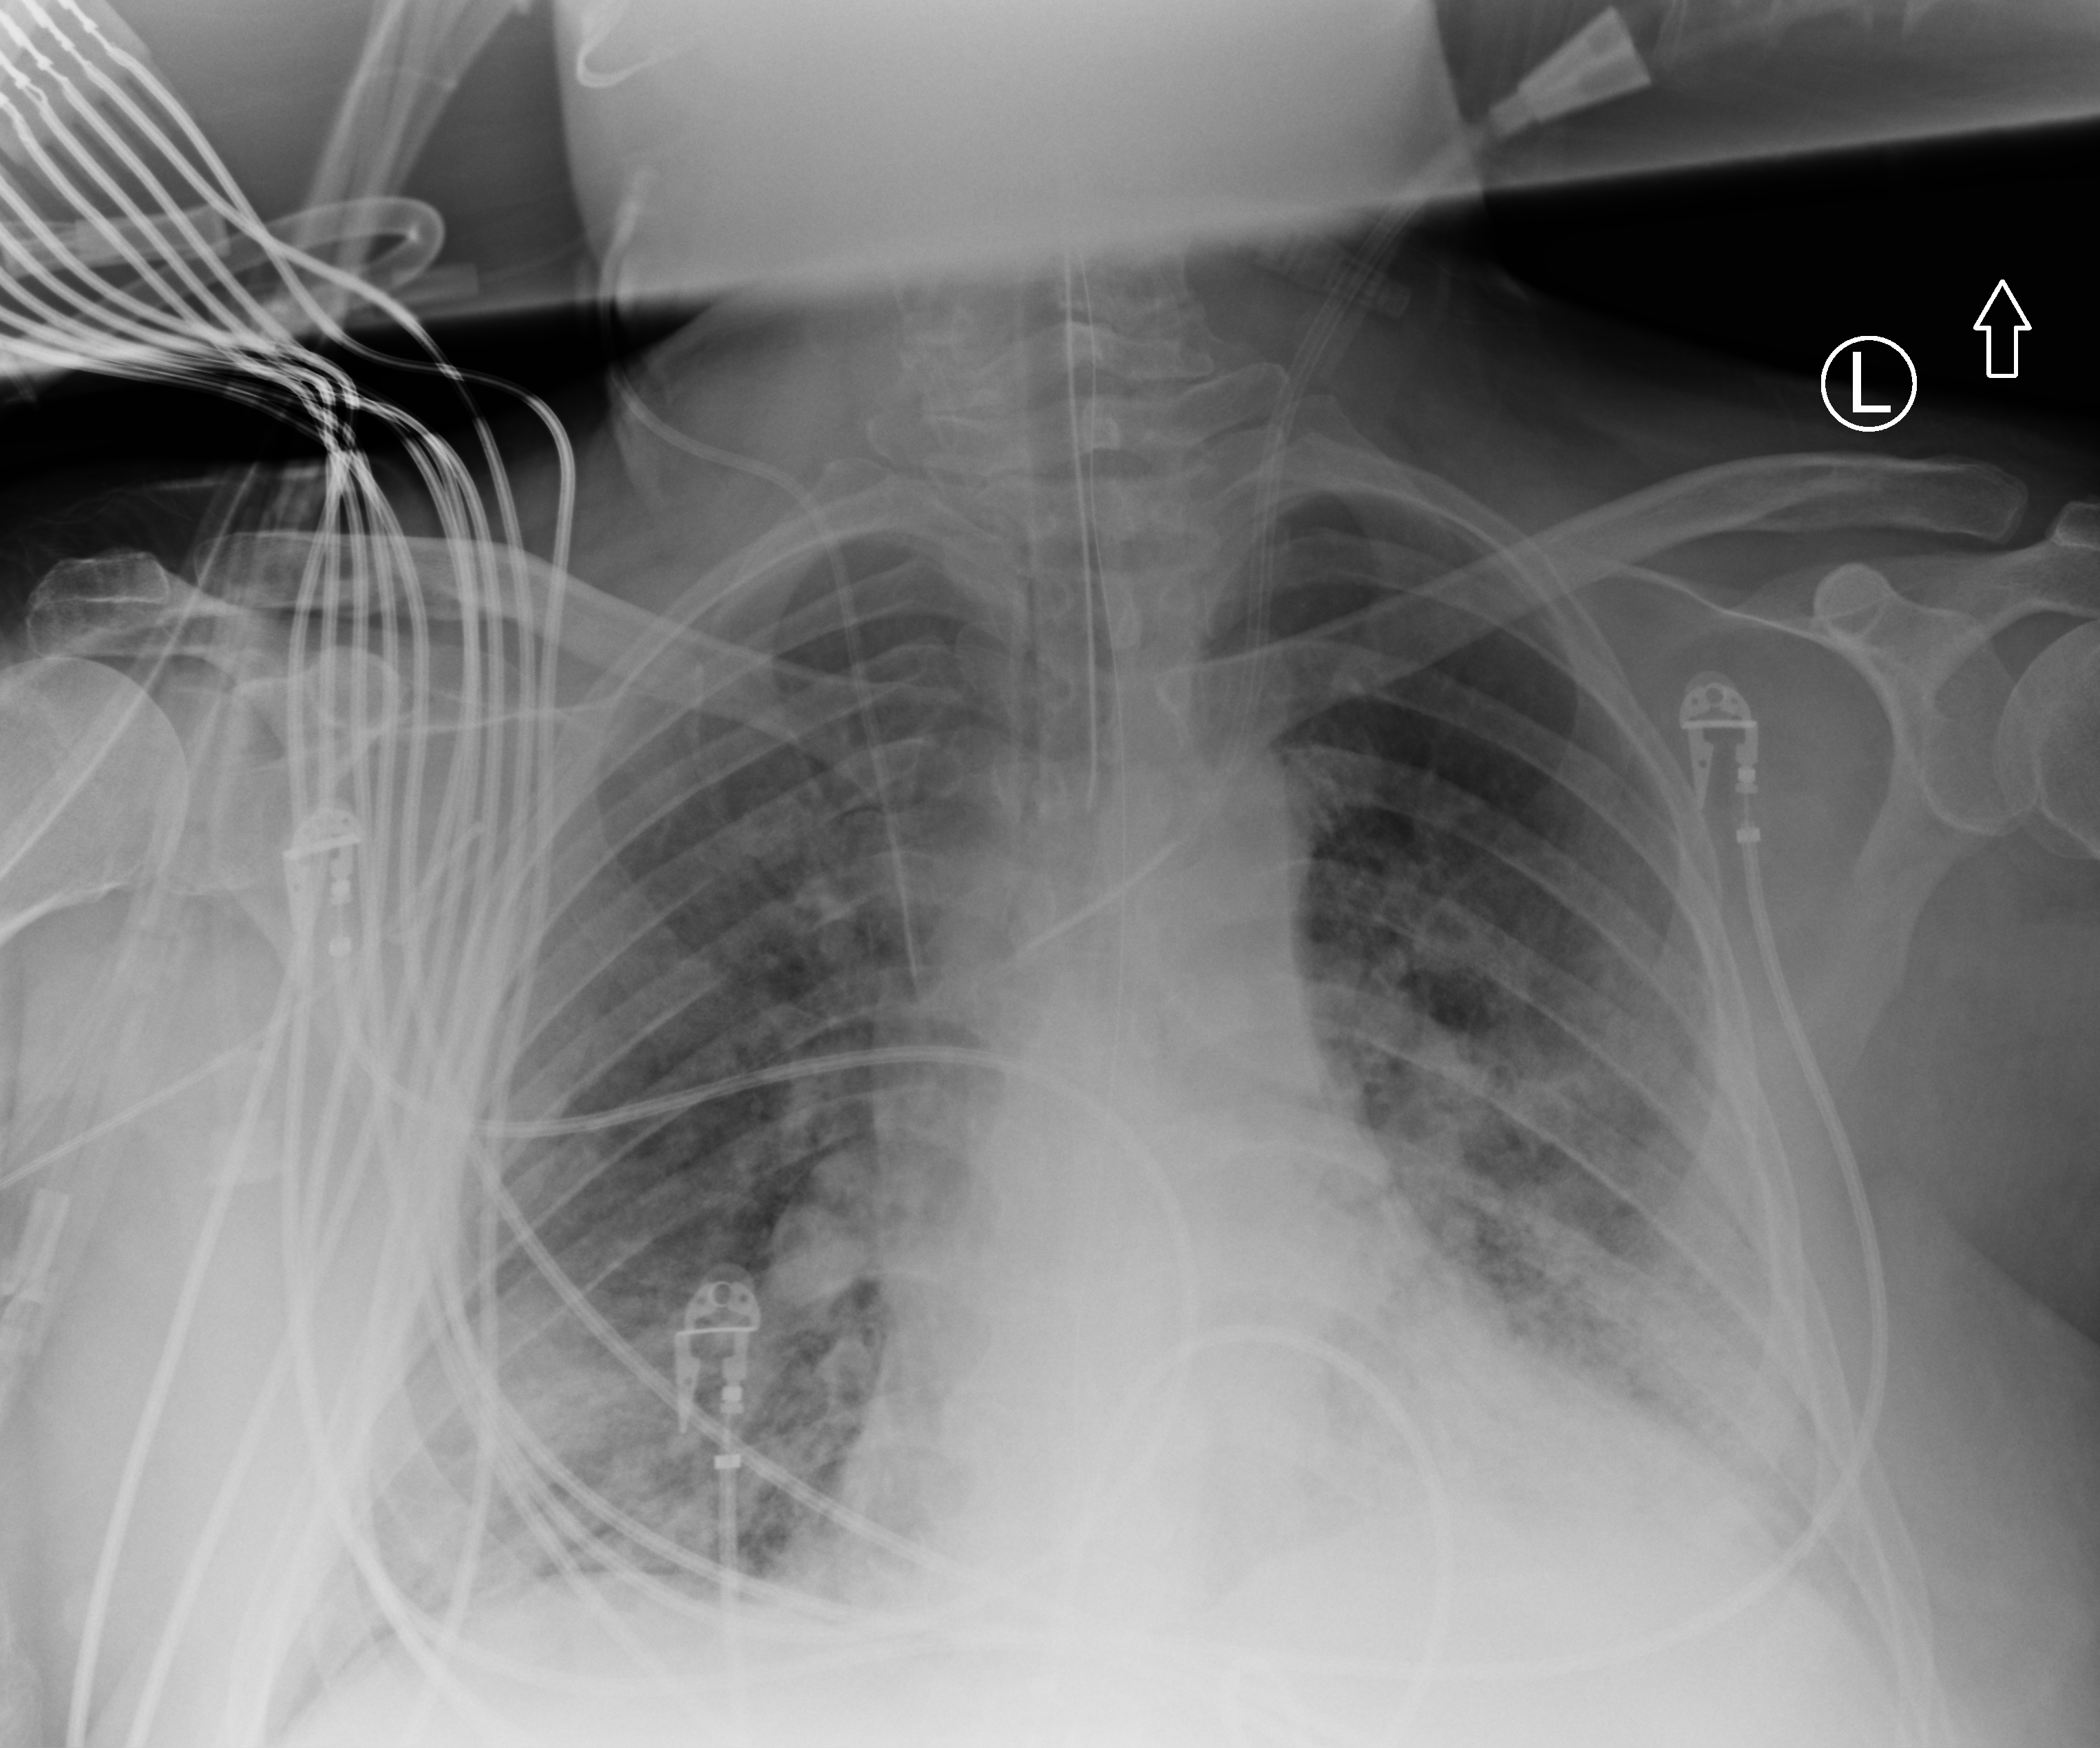
Chest X-ray (portable); anteroposterior (AP) projection. Patient hospitalised with COVID-19; male, aged 18–59 years.
From the hospital-stay record, not from the radiograph (when in the stay this image was taken is not recorded):
- mechanically ventilated during this hospital stay: yes